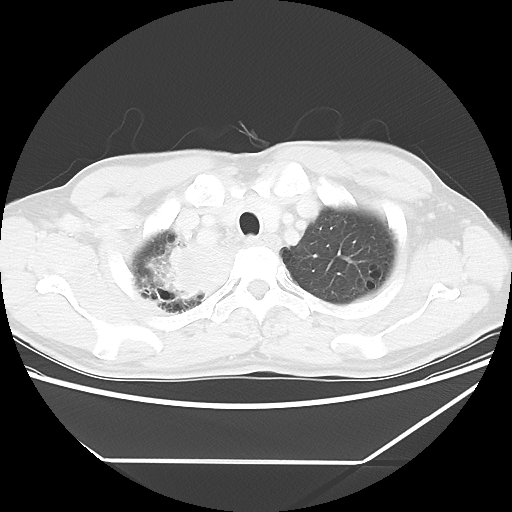
Chest CT, one axial slice. Slice 53 of 60 in the series (ordered by position). Reconstruction kernel LUNG. Lung window (W 1500 / L -600 HU). 5 mm slice thickness. 512 × 512 image matrix, field of view 367 × 367 mm. Male patient, age 58 years. From the clinical record (not read from this slice): clinical TNM (as recorded): T2 N2 M0.
Annotated regions visible in this slice (bounding box drawn by a radiologist):
- lung tumour (recorded histology: squamous cell carcinoma): bounding box (x1, y1, x2, y2) in pixels: (144, 233, 237, 313)